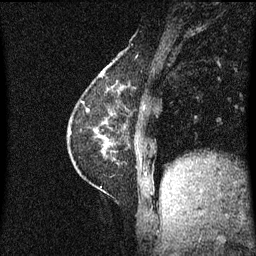
Breast MRI (dynamic contrast-enhanced), one sagittal slice; position 17 of 60 along the scan axis; dynamic contrast-enhanced series, image 2 of 3 at this slice position (ordered by acquisition); 1.5 T; TE 4.2 ms, TR 8.4 ms; 2 mm slice thickness; 256 × 256 image matrix, field of view 200 × 200 mm. Female patient, age 60 years.
Outlined on this slice (semi-automatic segmentation, software-assisted and operator-edited):
- analysis volume of interest (the breast-tissue region the enhancement analysis was run in; not a lesion): bounding box [x1, y1, x2, y2] px = [69, 66, 131, 193]
- tumour enhancement mask (voxels above the 70 % enhancement threshold inside the analysis volume of interest): [70, 66, 125, 157]